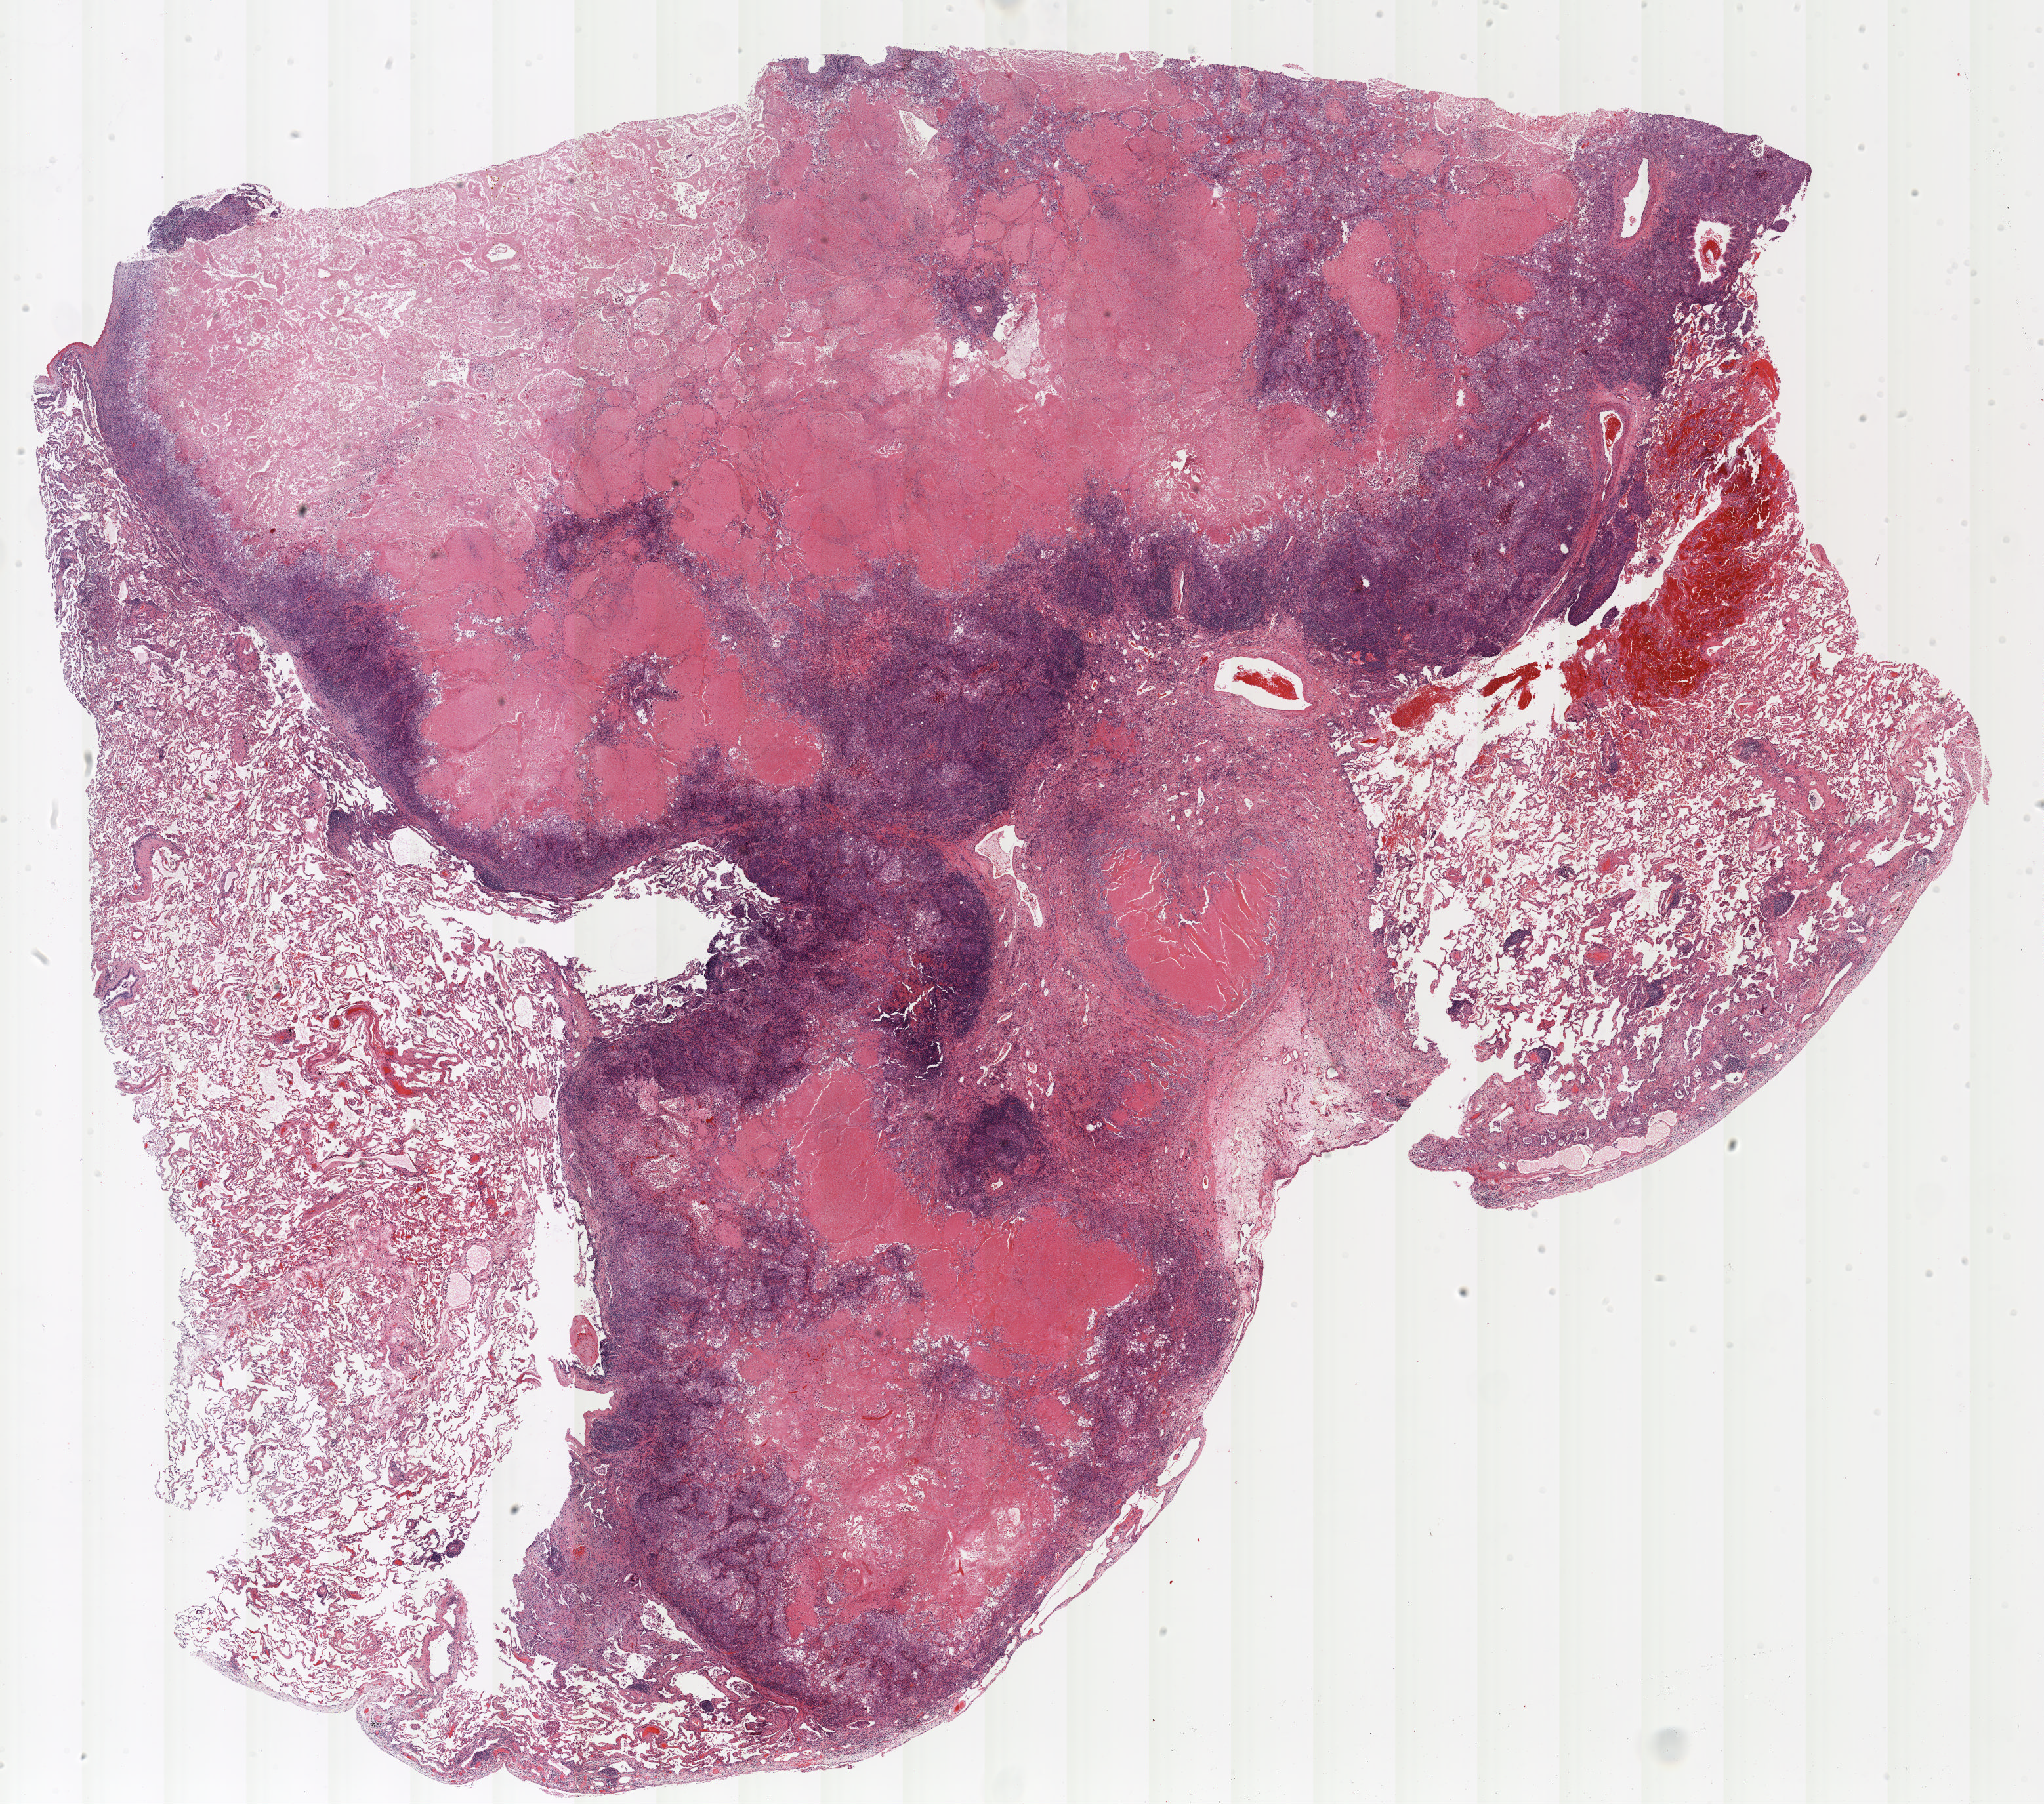
Whole-slide histology image, Hematoxylin and eosin (H&E) stained — shown as a low-resolution overview of the whole scanned area (about 25.0 x 22.1 mm, acquisition: 20x scan). Formalin-fixed paraffin-embedded (FFPE) section. Lung tissue. Female, age 67 at enrolment. Grade: poorly differentiated (G3).
Participant's lung-cancer diagnosis: Squamous cell carcinoma, NOS (ICD-O-3 8070/3). Stage (AJCC 6th edition): IA. Primary tumour location (clinical record): left upper lobe. Tumour size (pathology): 25 mm.